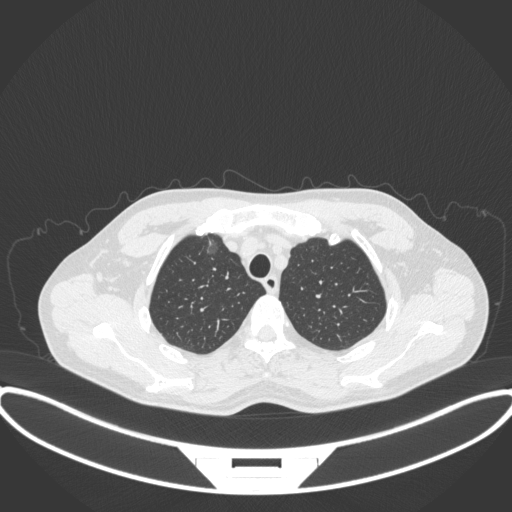
Chest CT, one axial slice. Position 306 of 395 along the scan axis. 120 kVp. Lung window (W 1500 / L -600 HU). 1 mm slice thickness. 512 × 512 image matrix, field of view 424 × 424 mm. Patient: male, 60 years. Case-level facts recorded for this patient, not image findings: clinical TNM (as recorded): T1c N0 M0.
Outlined on this slice (bounding box drawn by a radiologist):
- lung tumour (recorded histology: adenocarcinoma): bounding box <204,234,223,257> (left, top, right, bottom; pixels)